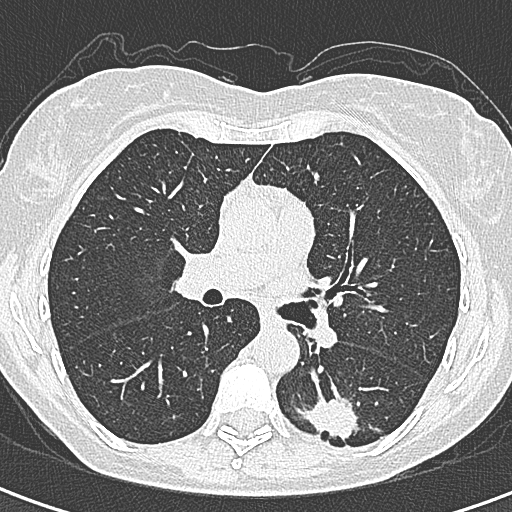
Low-dose screening chest CT, axial slice. First (baseline) screen. Lung window (W 1500 / L -600 HU). Lung (sharp) reconstruction kernel (B80f). 120 kVp. 512 × 512 image matrix. Female, age 58 years at enrolment.
Expert reader's lesion annotation, box from (x=296, y=387) to (x=366, y=455) px. The screening reader recorded 2 non-calcified nodules or masses ≥4 mm on this exam; which of them this box marks is not recorded. Participant outcome: lung cancer diagnosed 22 days after this screen — adenocarcinoma, NOS, left lower lobe, moderately differentiated (G2), stage IA (AJCC 6th edition), 25 mm at pathology.